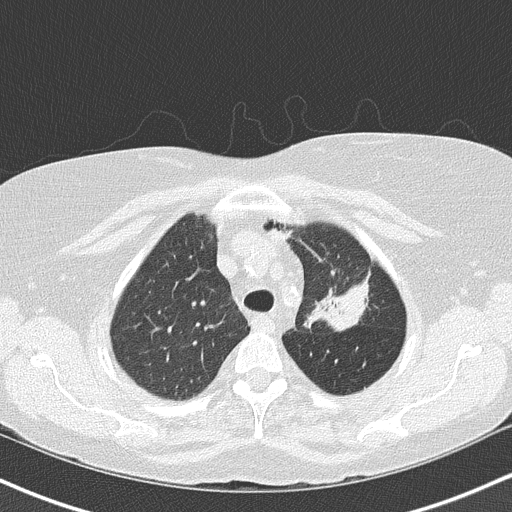
Chest CT (low-dose screening protocol), one axial image. Third screening round (two years after baseline). Lung window (W 1500 / L -600 HU). 2 mm slice thickness. Slice 121 of 147 in the series. 512 × 512 image matrix, field of view 320 × 320 mm. Female, age 68 years at enrolment. Former smoker at enrolment.
Lesion marked by an expert reader, box from (x=292, y=228) to (x=380, y=335) px. Reader record for this screening exam (exam-level; its link to the box is not recorded): non-calcified nodule or mass ≥4 mm, left upper lobe, 5 × 5 mm, poorly defined margins, mixed attenuation, pre-existing on the prior screen: yes; interval growth: yes. Lung cancer was diagnosed 42 days after this screen: adenocarcinoma, NOS, left upper lobe, poorly differentiated (G3), stage IB (AJCC 6th edition), 50 mm at pathology.